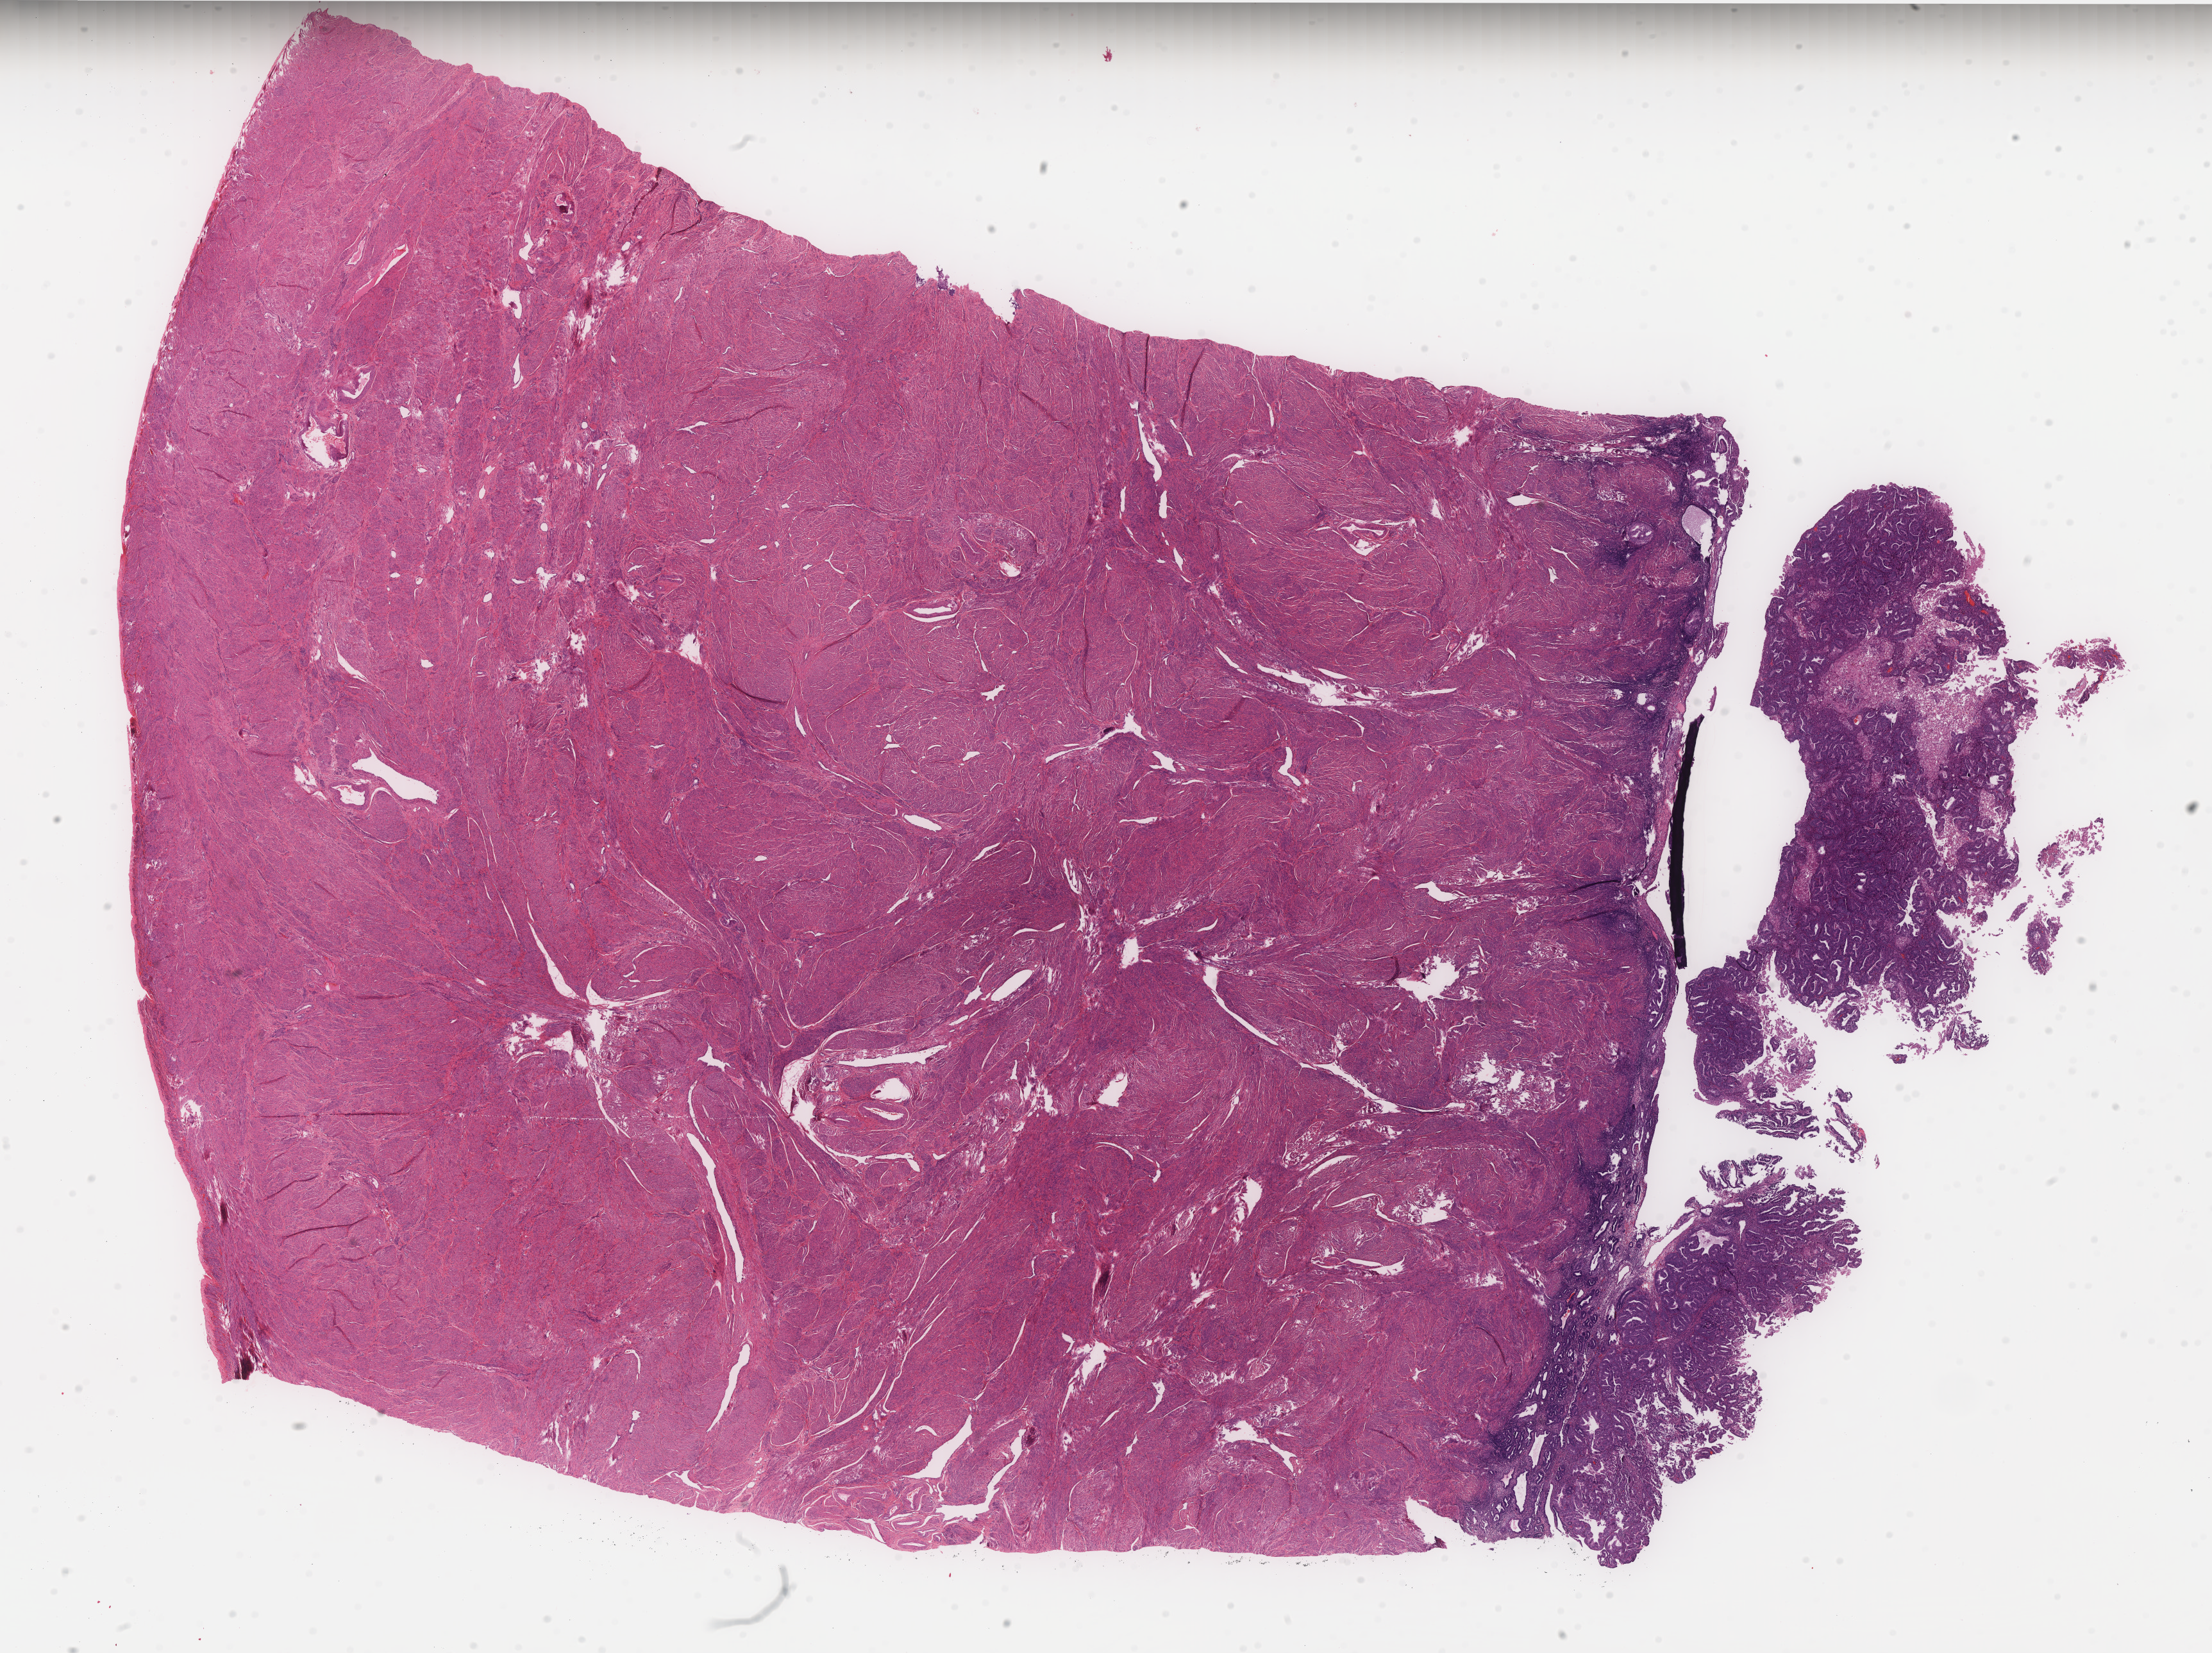
Hematoxylin and eosin (H&E) stained whole-slide image — low-resolution overview of the scanned area, about 27.7 x 20.7 mm. FFPE section. Primary tumour sample from the uterus. Female, age 53 years at initial diagnosis. Histologic grade: G2 (moderately differentiated).
FIGO stage: IA. Diagnosis: Endometrioid adenocarcinoma, NOS.